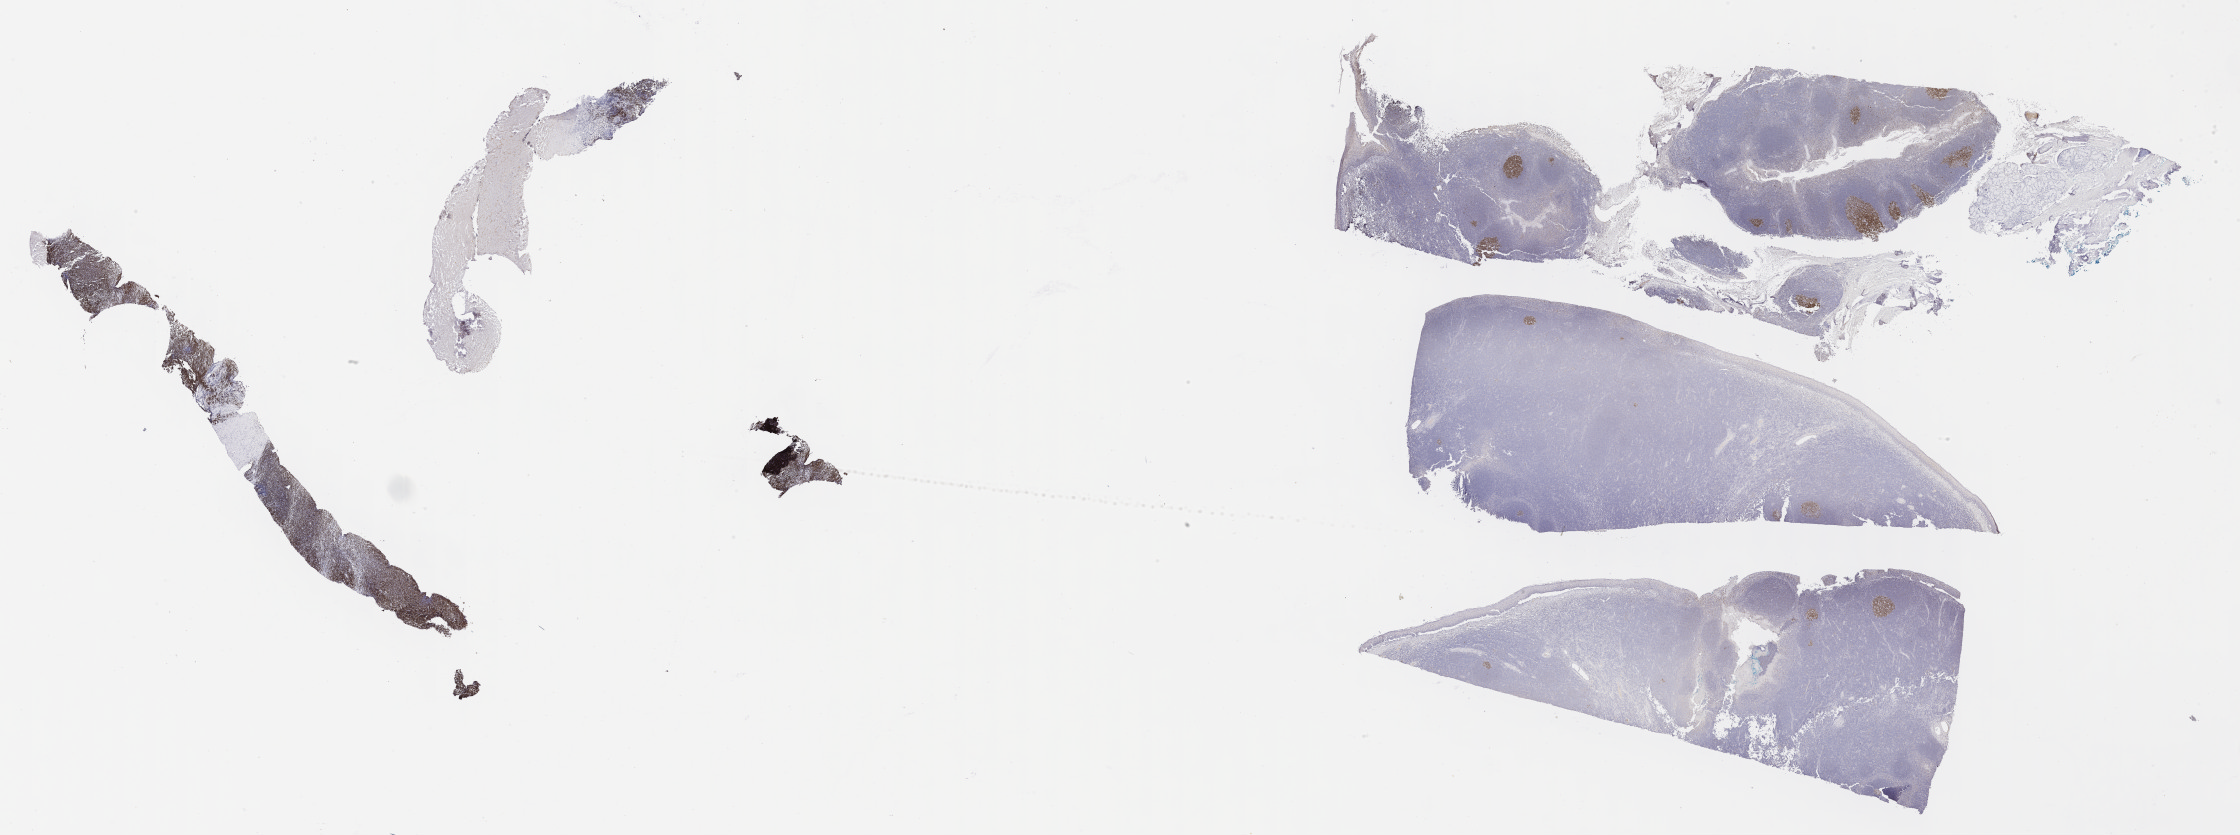
Immunohistochemistry (IHC) whole-slide image stained for BCL6, whole scanned area (about 36.2 x 13.5 mm) shown as a low-resolution overview, tumor tissue. Patient male; aged 10.
Histologic diagnosis: Burkitt lymphoma, NOS.